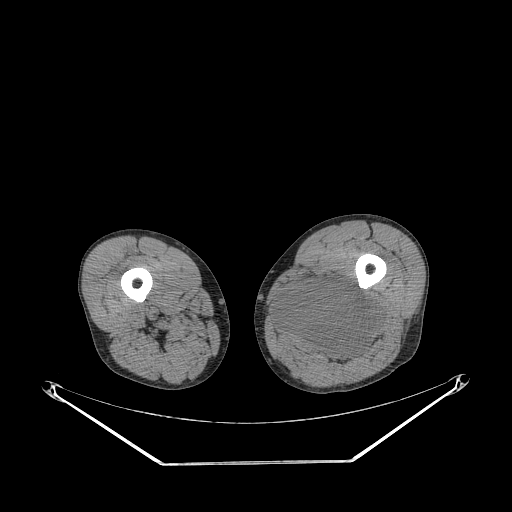
CT of an extremity soft-tissue mass (from a PET/CT study), one axial slice; position 233 of 267 along the scan axis; 140 kVp; soft-tissue window (W 400 / L 40 HU); 3.75 mm slice thickness; 512 × 512 image matrix. Male patient. From the clinical record (not read from this slice): histological type: undifferentiated pleomorphic liposarcoma; grade: high; site of the primary tumour: left thigh.
Structures marked on this image (expert contour drawn on MRI and transferred to this co-registered scan by the dataset authors):
- gross tumour volume including surrounding oedema: bounding box <276,279,380,362> (left, top, right, bottom; pixels)
- gross tumour volume (mass): <276,279,380,360>